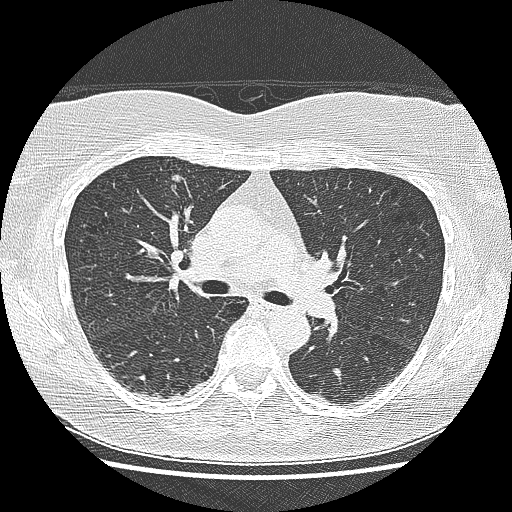
Low-dose screening chest CT, one axial slice; position 92 of 155 along the scan axis; reconstruction kernel LUNG; 120 kVp; lung window (W 1500 / L -600 HU); 2.5 mm slice thickness; 512 × 512 image matrix, field of view 330 × 330 mm.
Outlined on this slice (outlined manually by an expert reader):
- lesion 1 (tumor, upper lobe of right lung): box from (x=172, y=175) to (x=181, y=182) px